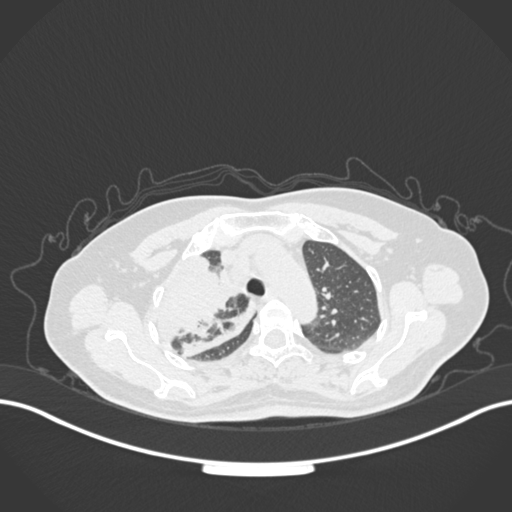
Chest CT, one axial slice. Position 123 of 177 along the scan axis. Reconstruction kernel B30f. 120 kVp. Lung window (W 1500 / L -600 HU). 1 mm slice thickness. 512 × 512 image matrix. Female patient, age 60 years. Case-level facts recorded for this patient, not image findings: clinical TNM (as recorded): T3 N1 M1.
Outlined on this slice (rectangle marked by the reading radiologist):
- lung tumour (recorded histology: adenocarcinoma): box from (x=150, y=253) to (x=238, y=353) px